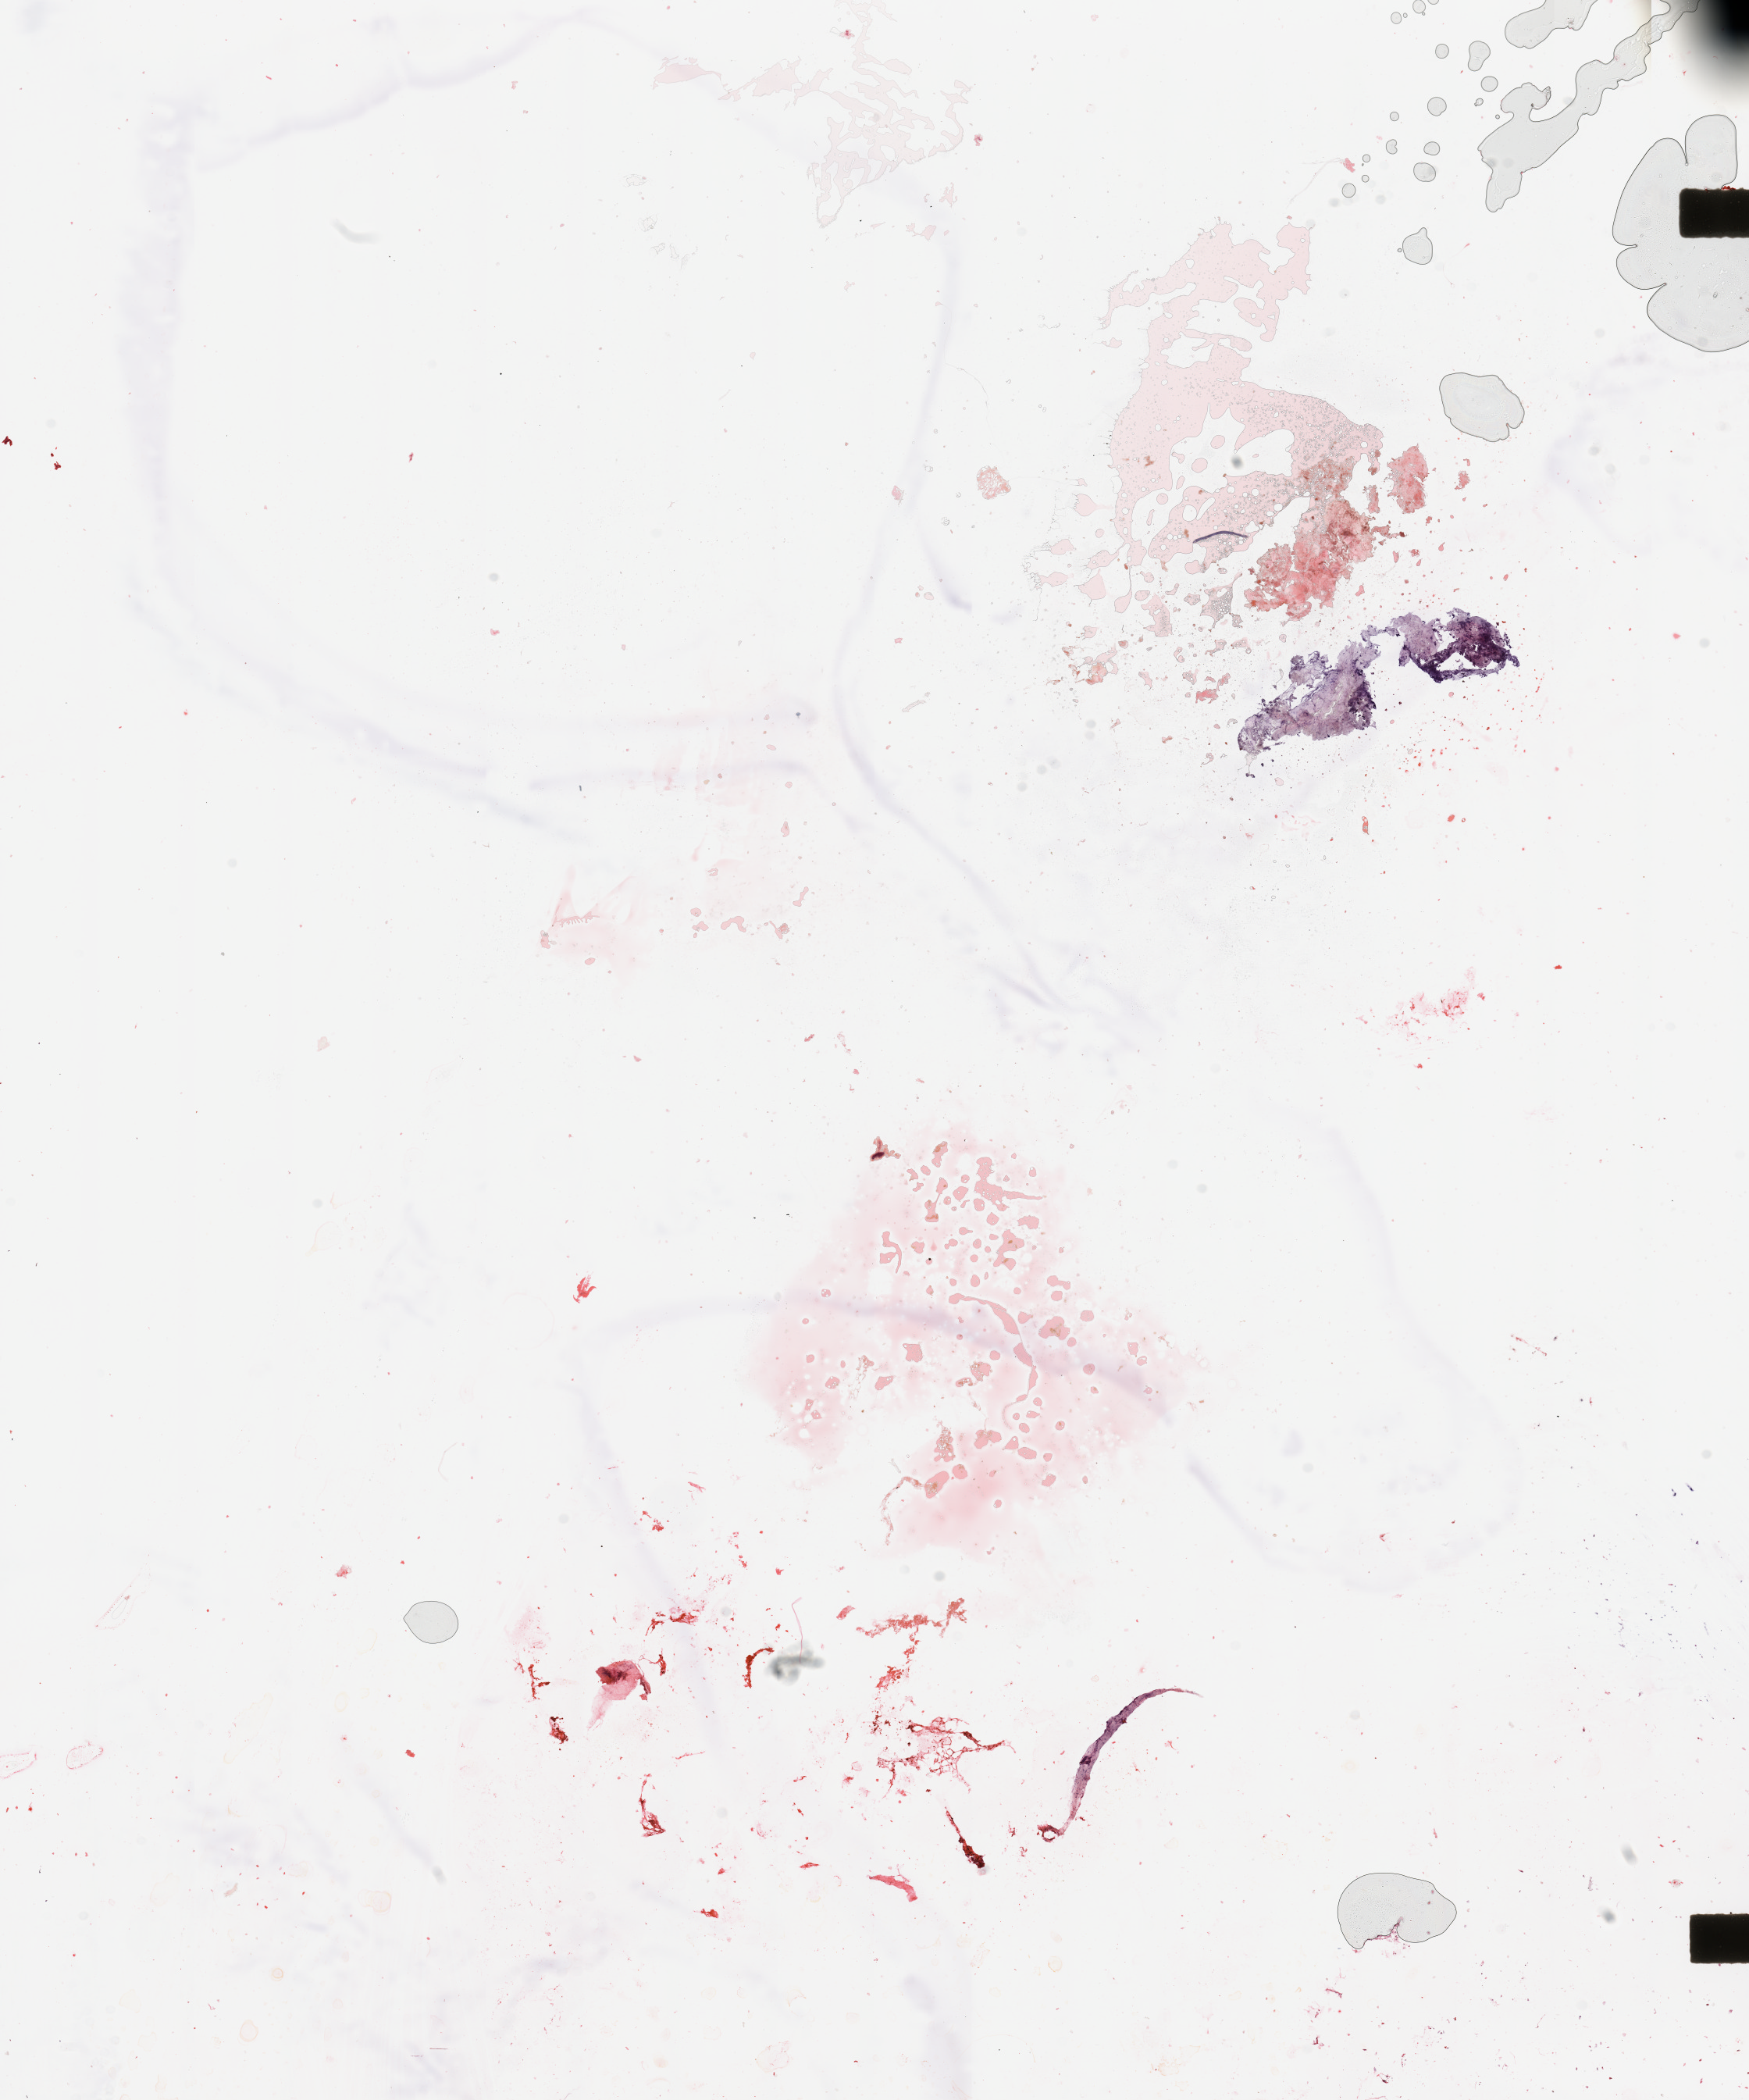
Digitized H&E tissue section (whole slide), a low-resolution overview of the entire scanned area, about 17.7 x 21.3 mm; normal (non-tumour) tissue (melanoma cohort); sampled site not recorded. Patient: female, age 51 years.
• this section: normal (non-tumour) tissue from the same patient
• patient diagnosis (cohort enrolment): cutaneous melanoma (skin)